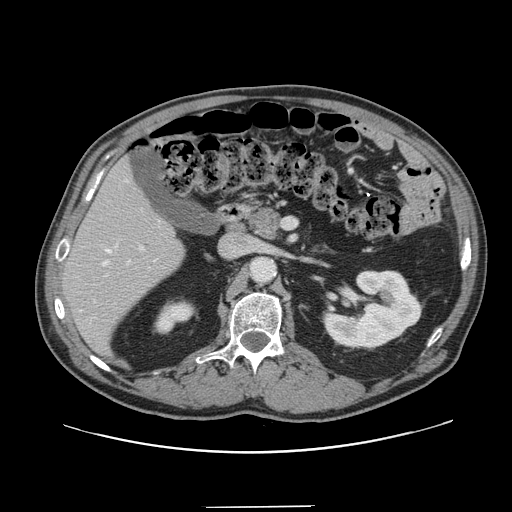
Contrast-enhanced abdominal CT, one axial slice. Slice 74 of 139 in the series (ordered by position). 120 kVp. Intravenous contrast given. Soft-tissue window (W 400 / L 40 HU). 2.5 mm slice thickness. 512 × 512 image matrix, field of view 397 × 397 mm. Male patient, age 64 years. Case-level facts recorded for this patient, not image findings: diagnosis: colorectal cancer liver metastases, imaged before liver resection; multiple liver metastases: yes; largest metastasis: 3.5 cm; chemotherapy before resection: yes.
Annotated regions visible in this slice (manually delineated by an expert):
- hepatic veins: bounding box (x1, y1, x2, y2) in pixels: (103, 180, 131, 266)
- liver: (64, 163, 183, 353)
- planned liver remnant (the part of the liver to remain after resection): (63, 162, 184, 353)
- portal vein (with intrahepatic branches): (106, 246, 143, 276)